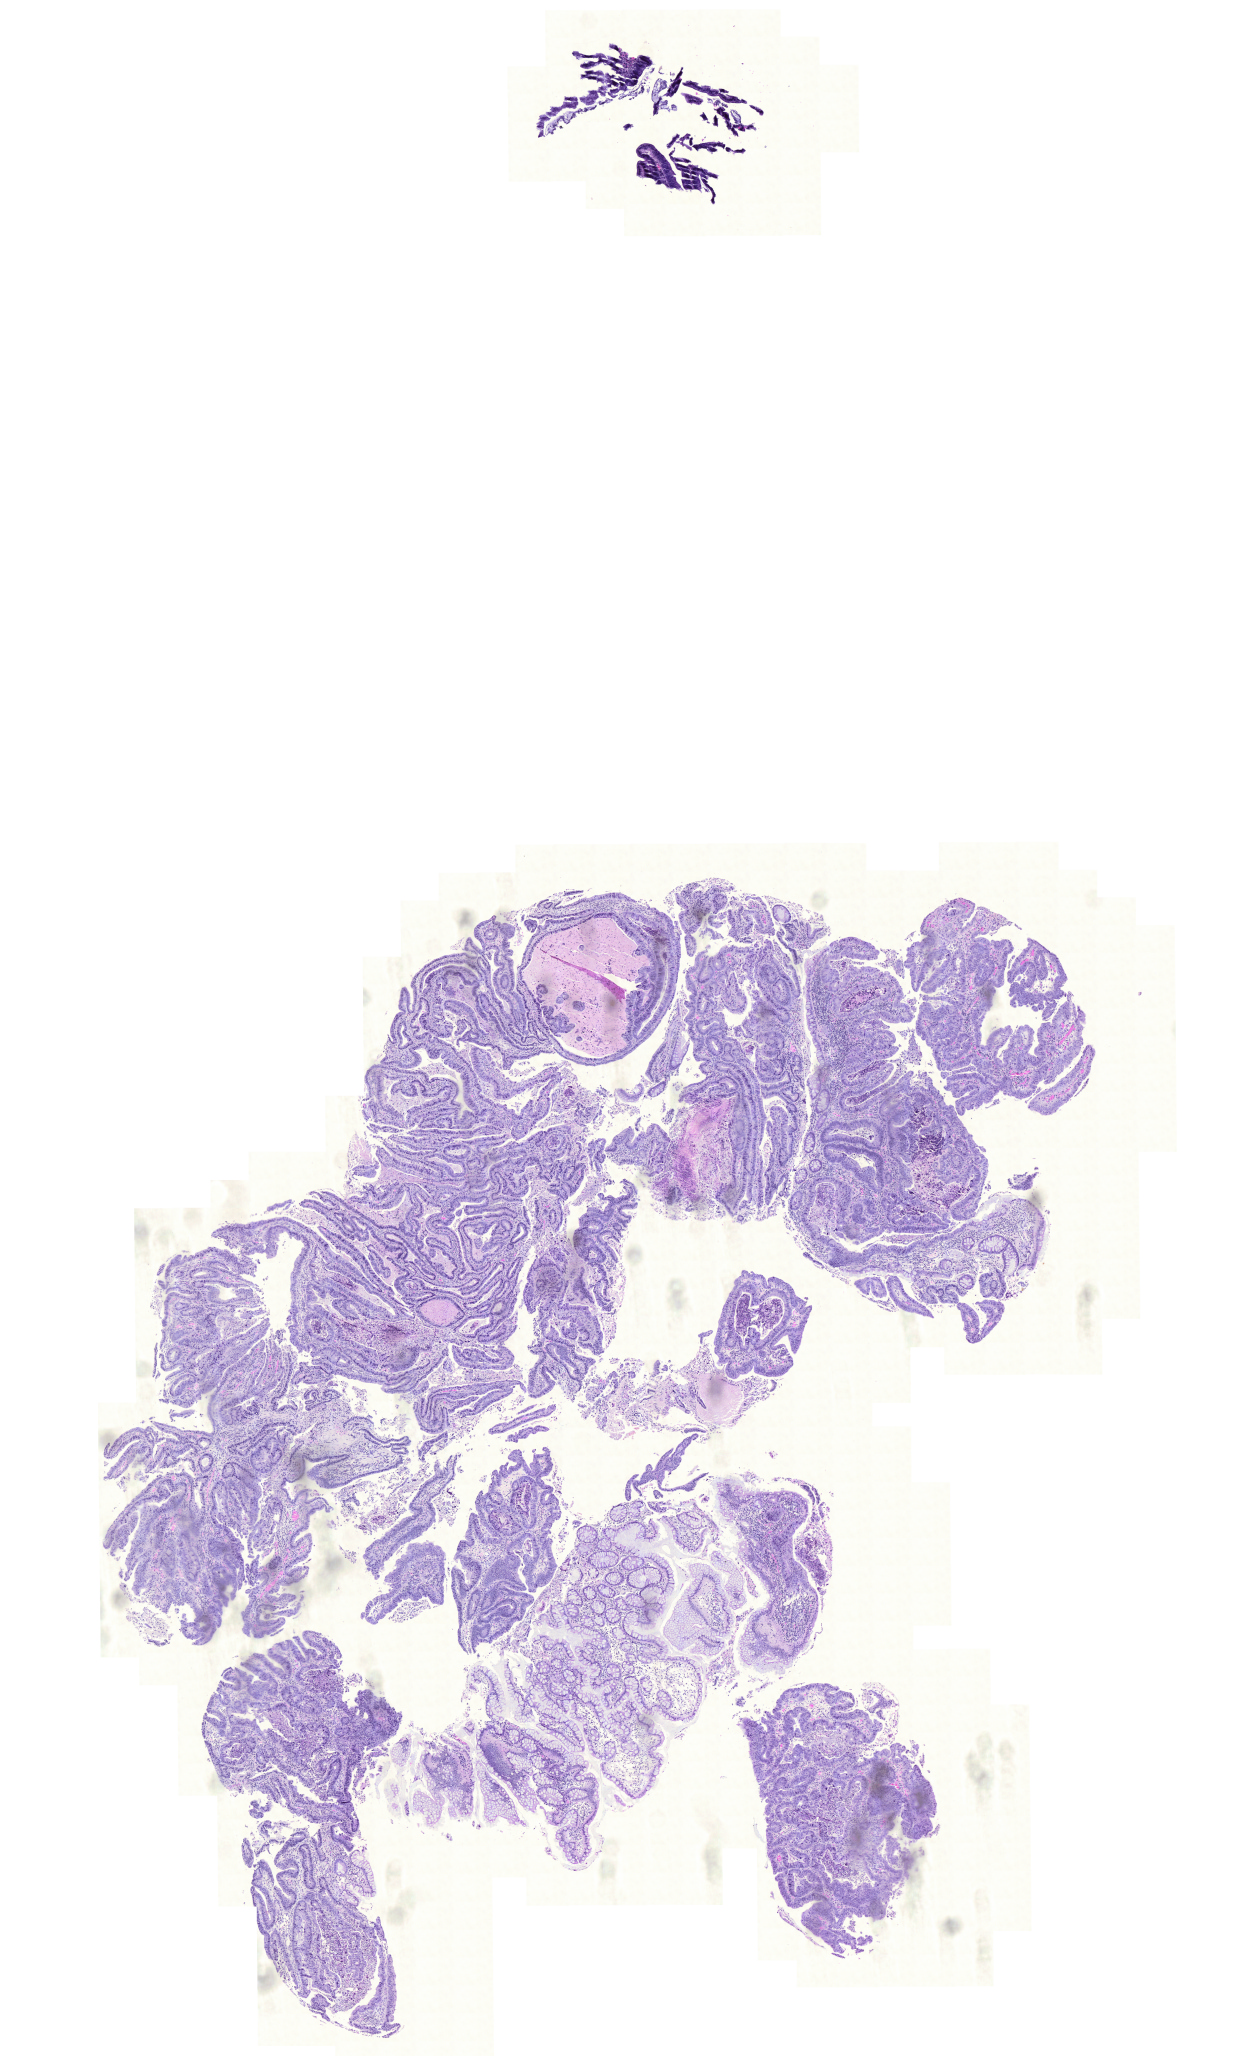
Whole-slide histology image, Hematoxylin and eosin (H&E) stained, low-resolution overview of the scanned area, about 9.3 x 15.3 mm (from a 20x scan), formalin-fixed paraffin-embedded (FFPE) diagnostic section, primary tumour sample from the colon. Male, age 66 years at initial diagnosis.
Diagnosis: Adenocarcinoma, NOS (transverse colon).